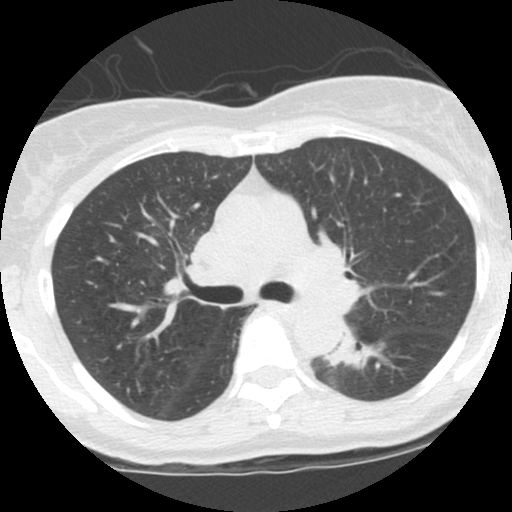
Low-dose screening chest CT, one axial slice. Slice 70 of 115 in the series (ordered by position). Reconstruction kernel STANDARD. Lung window (W 1500 / L -600 HU). 2.5 mm slice thickness. 512 × 512 image matrix, field of view 290 × 290 mm.
Annotated regions visible in this slice (expert manual segmentation):
- lesion 1 (tumor, lower lobe of left lung): bounding box (x1, y1, x2, y2) in pixels: (324, 336, 373, 367)